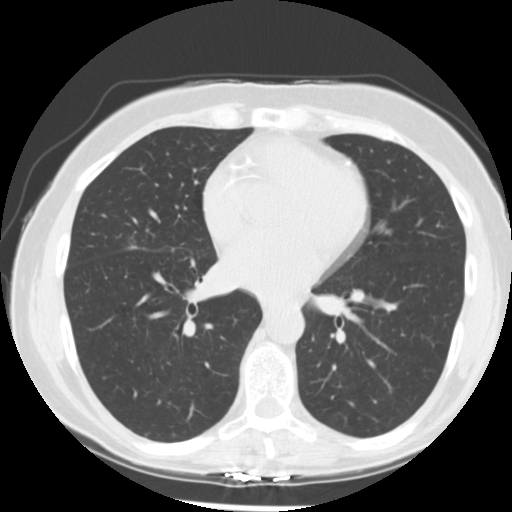
Low-dose screening chest CT, one axial slice; slice 125 of 255 in the series (ordered by position); lung window (W 1500 / L -600 HU); 2.5 mm slice thickness; 512 × 512 image matrix, field of view 320 × 320 mm.
Outlined on this slice (expert manual segmentation):
- lesion 1 (tumor, middle lobe of right lung): bounding box (x1, y1, x2, y2) in pixels: (131, 246, 137, 249)